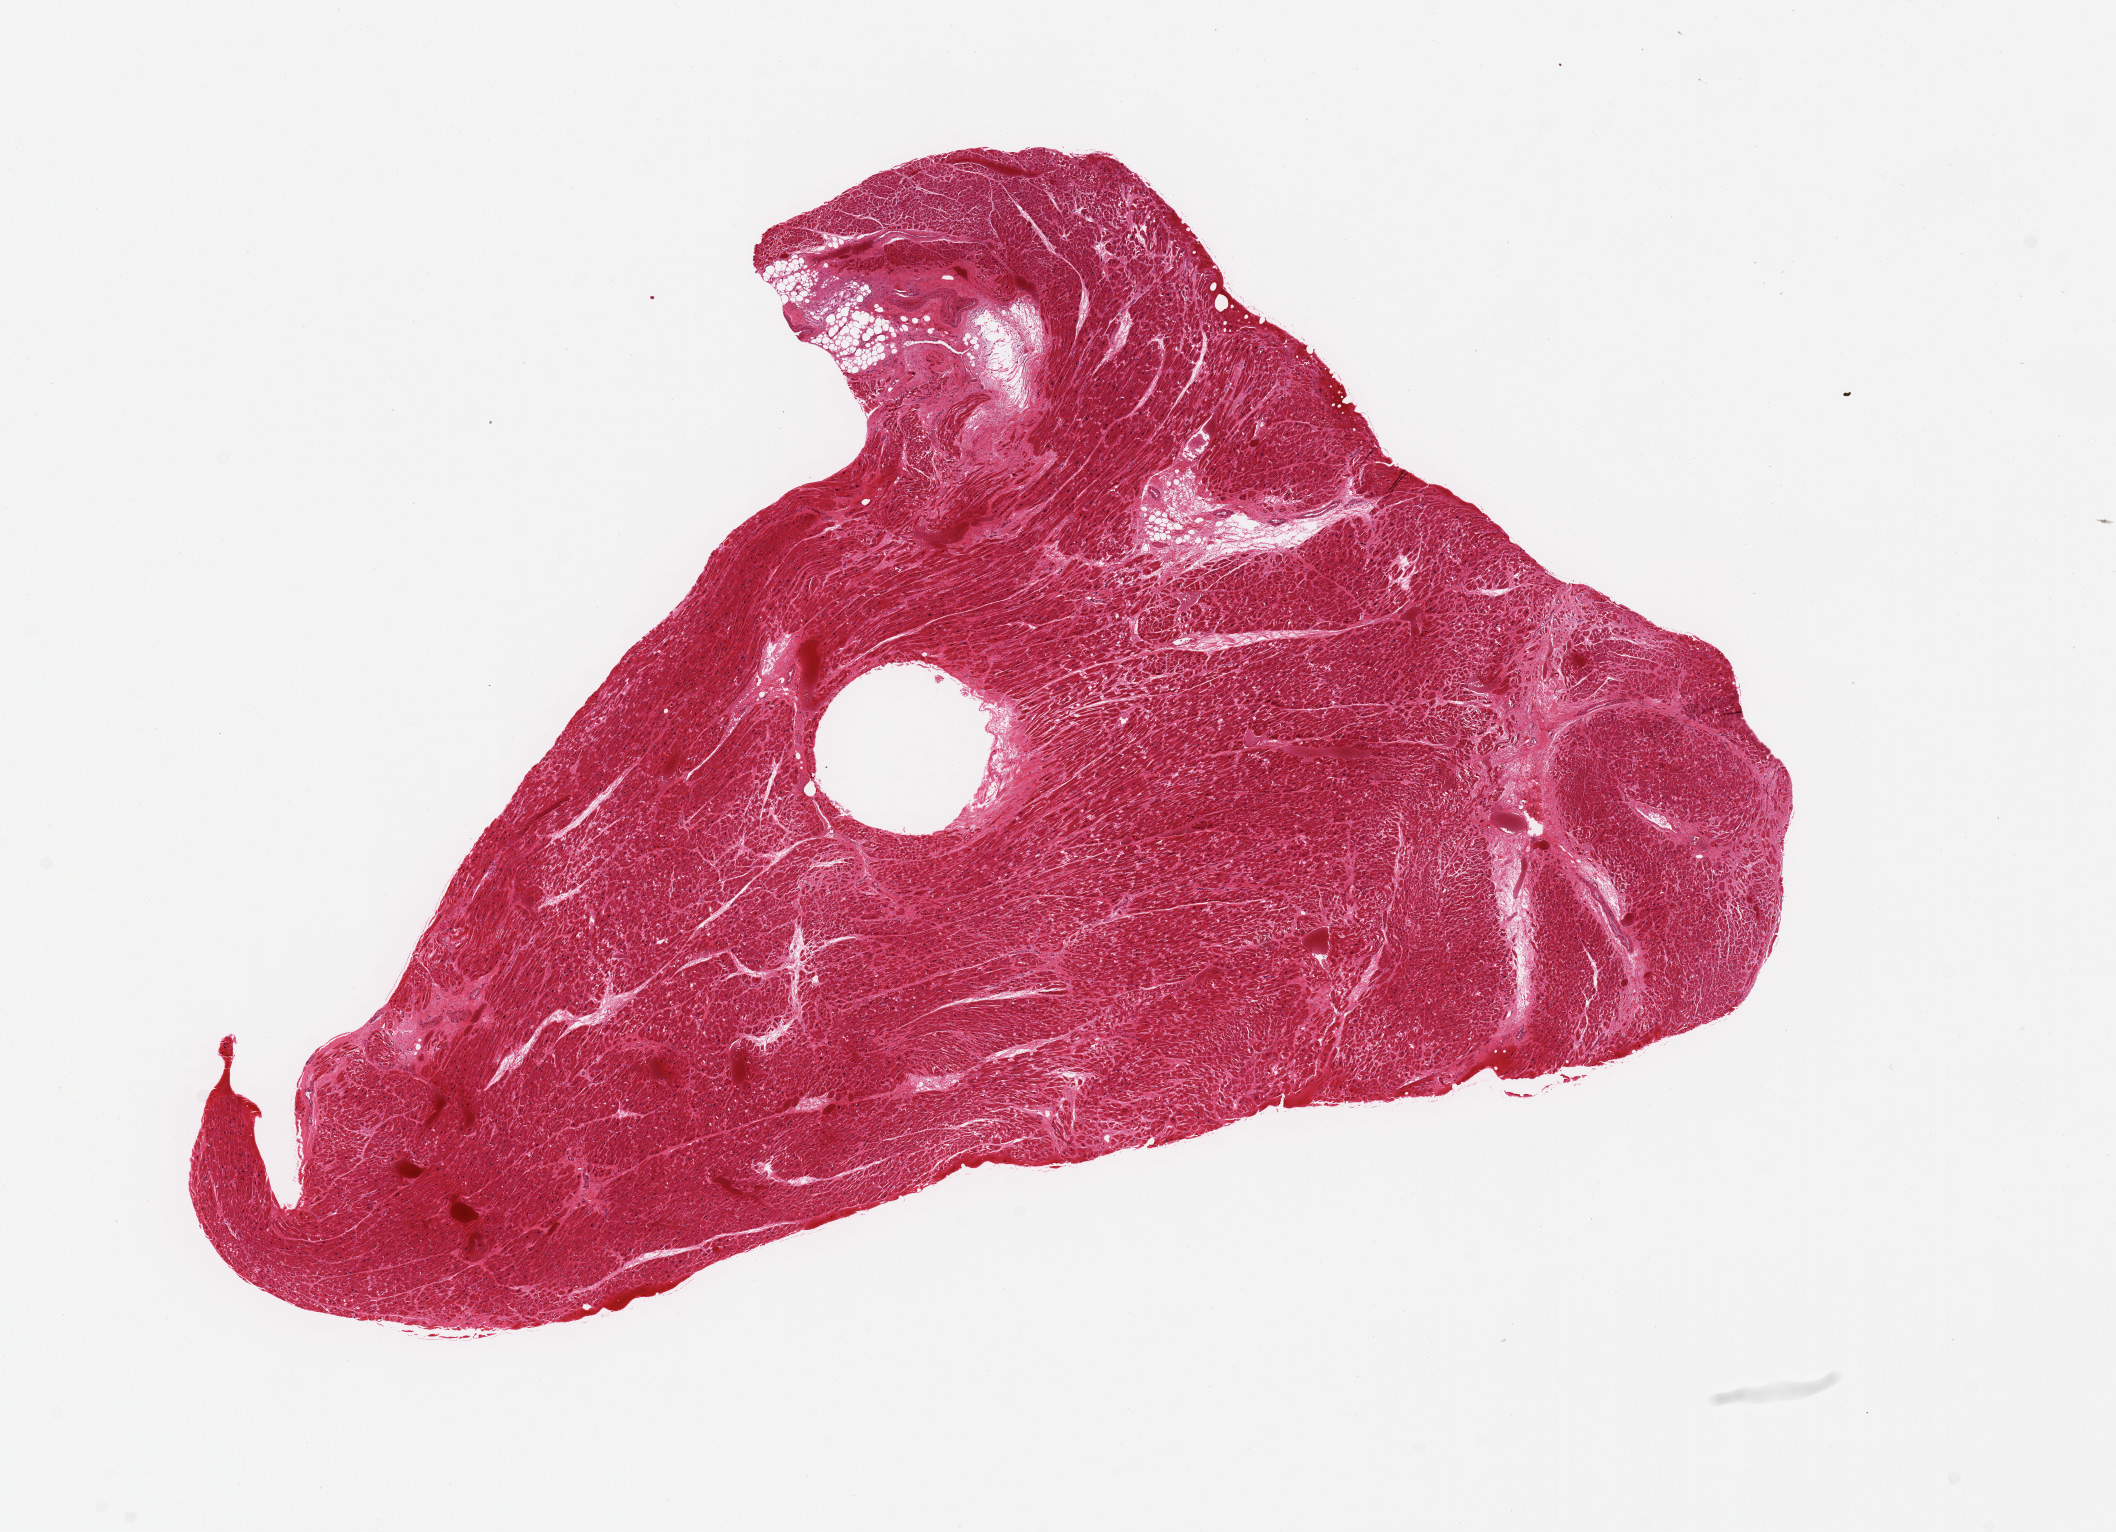
Whole-slide image, H&E stain — low-resolution overview of the scanned area, about 16.7 x 12.1 mm. PAXgene-fixed paraffin-embedded (PFPE) section. Target tissue: heart. Tissue donor sample. Donor: male.
Reviewer comment on this tissue sample: 11x8 mm; moderate congestion; patchy fibrosis.